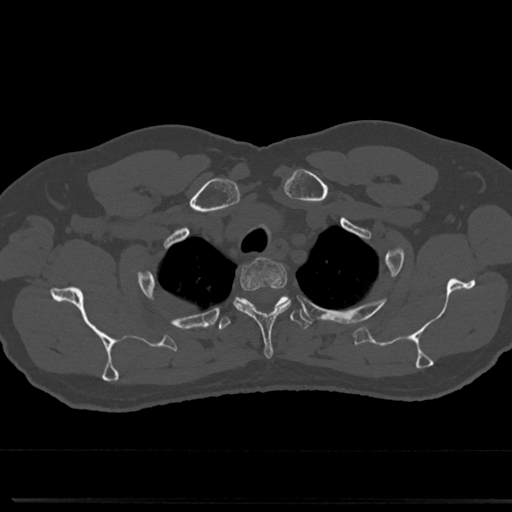
CT including the spine, one axial slice; slice 619 of 817 in the series (ordered by position); reconstruction kernel Br40s/3; 120 kVp; bone window (W 1800 / L 400 HU); 0.5 mm slice thickness; 512 × 512 image matrix, field of view 355 × 355 mm. Patient: male, 61 years. Case-level facts recorded for this patient, not image findings: primary cancer: prostate.
Outlined on this slice (semi-automatically segmented with operator editing):
- T2 vertebra: bounding box [x1, y1, x2, y2] px = [235, 260, 288, 342]
- T3 vertebra: [215, 293, 313, 333]